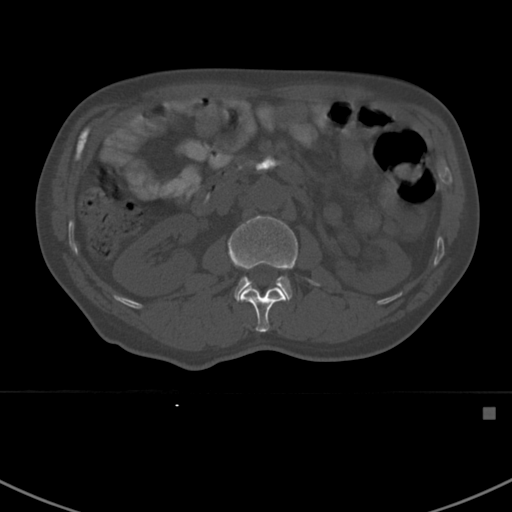
CT including the spine, one axial slice. Position 297 of 412 along the scan axis. 120 kVp. Bone window (W 1800 / L 400 HU). 1.5 mm slice thickness. 512 × 512 image matrix. Patient: male, 59 years. From the clinical record (not read from this slice): primary cancer: prostate.
Structures marked on this image (semi-automatic segmentation, software-assisted and operator-edited):
- L1 vertebra: bounding box [x1, y1, x2, y2] px = [241, 286, 286, 332]
- L2 vertebra: [228, 215, 321, 302]